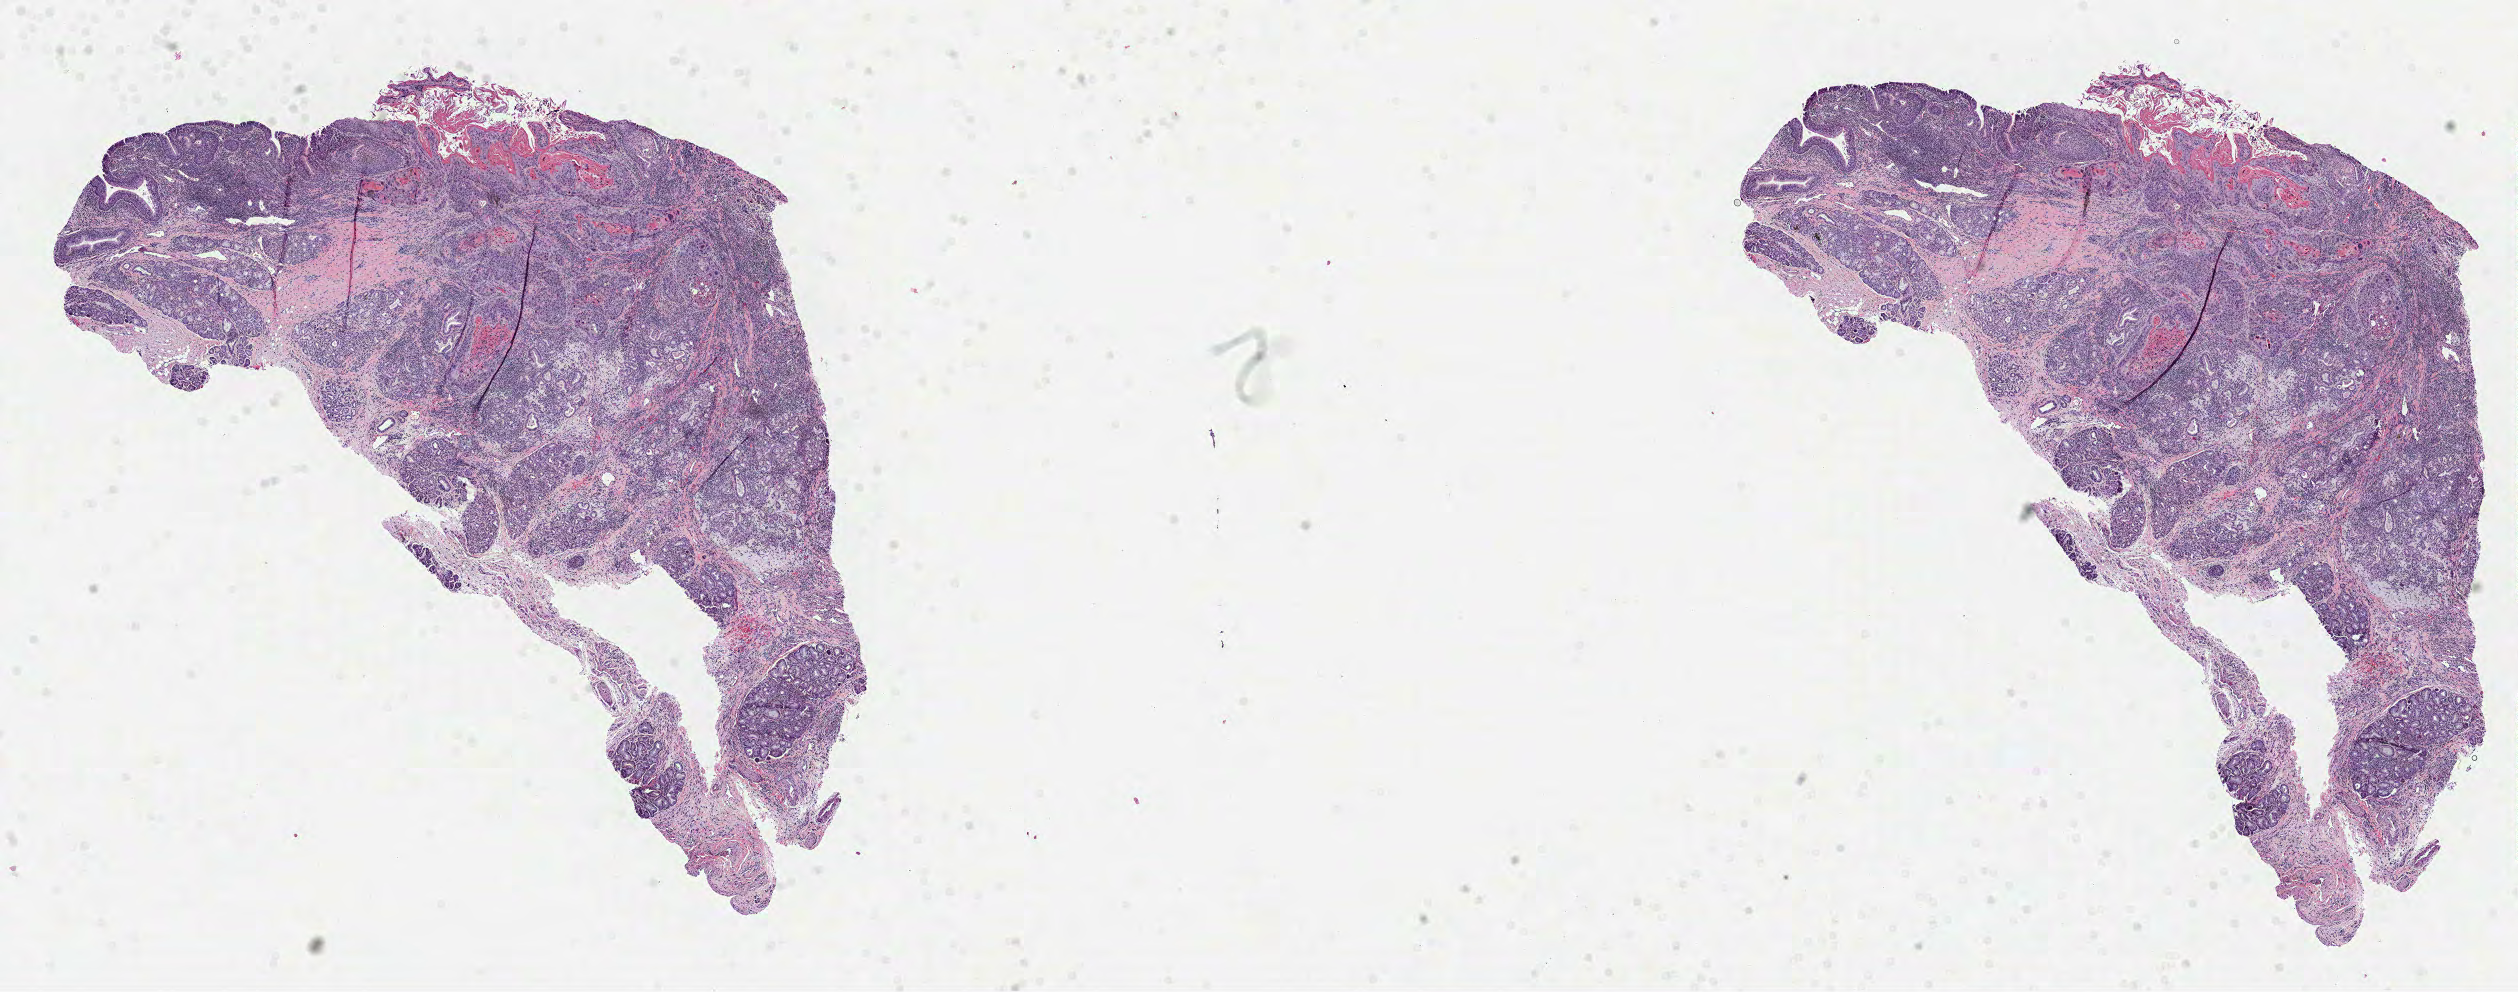
H&E whole-slide image, low-resolution overview of the scanned area, about 20.3 x 8.0 mm (from a 40x scan), formalin-fixed paraffin-embedded (FFPE) diagnostic section, primary tumour sample from the head and neck. Patient: male, age at initial diagnosis 64 years. Histologic grade: G2 (moderately differentiated).
Diagnosis: Squamous cell carcinoma, NOS (larynx, NOS). AJCC pathologic stage: IVA (7th edition). Lymph nodes positive (case pathology): 0 of 27 examined.